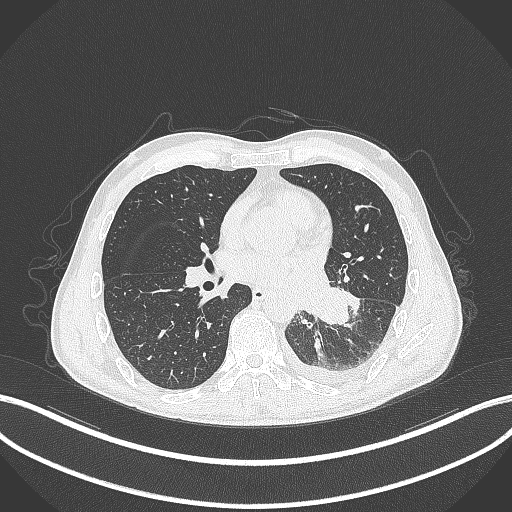
Chest CT, one axial slice; position 147 of 295 along the scan axis; reconstruction kernel B70f; 120 kVp; lung window (W 1500 / L -600 HU); 1 mm slice thickness; 512 × 512 image matrix, field of view 400 × 400 mm. Patient: male, 47 years. From the clinical record (not read from this slice): clinical TNM (as recorded): T3 N1 M1c; histopathological grade: G3.
Structures marked on this image (rectangle marked by the reading radiologist):
- lung tumour (recorded histology: small cell carcinoma): box from (x=310, y=285) to (x=350, y=326) px